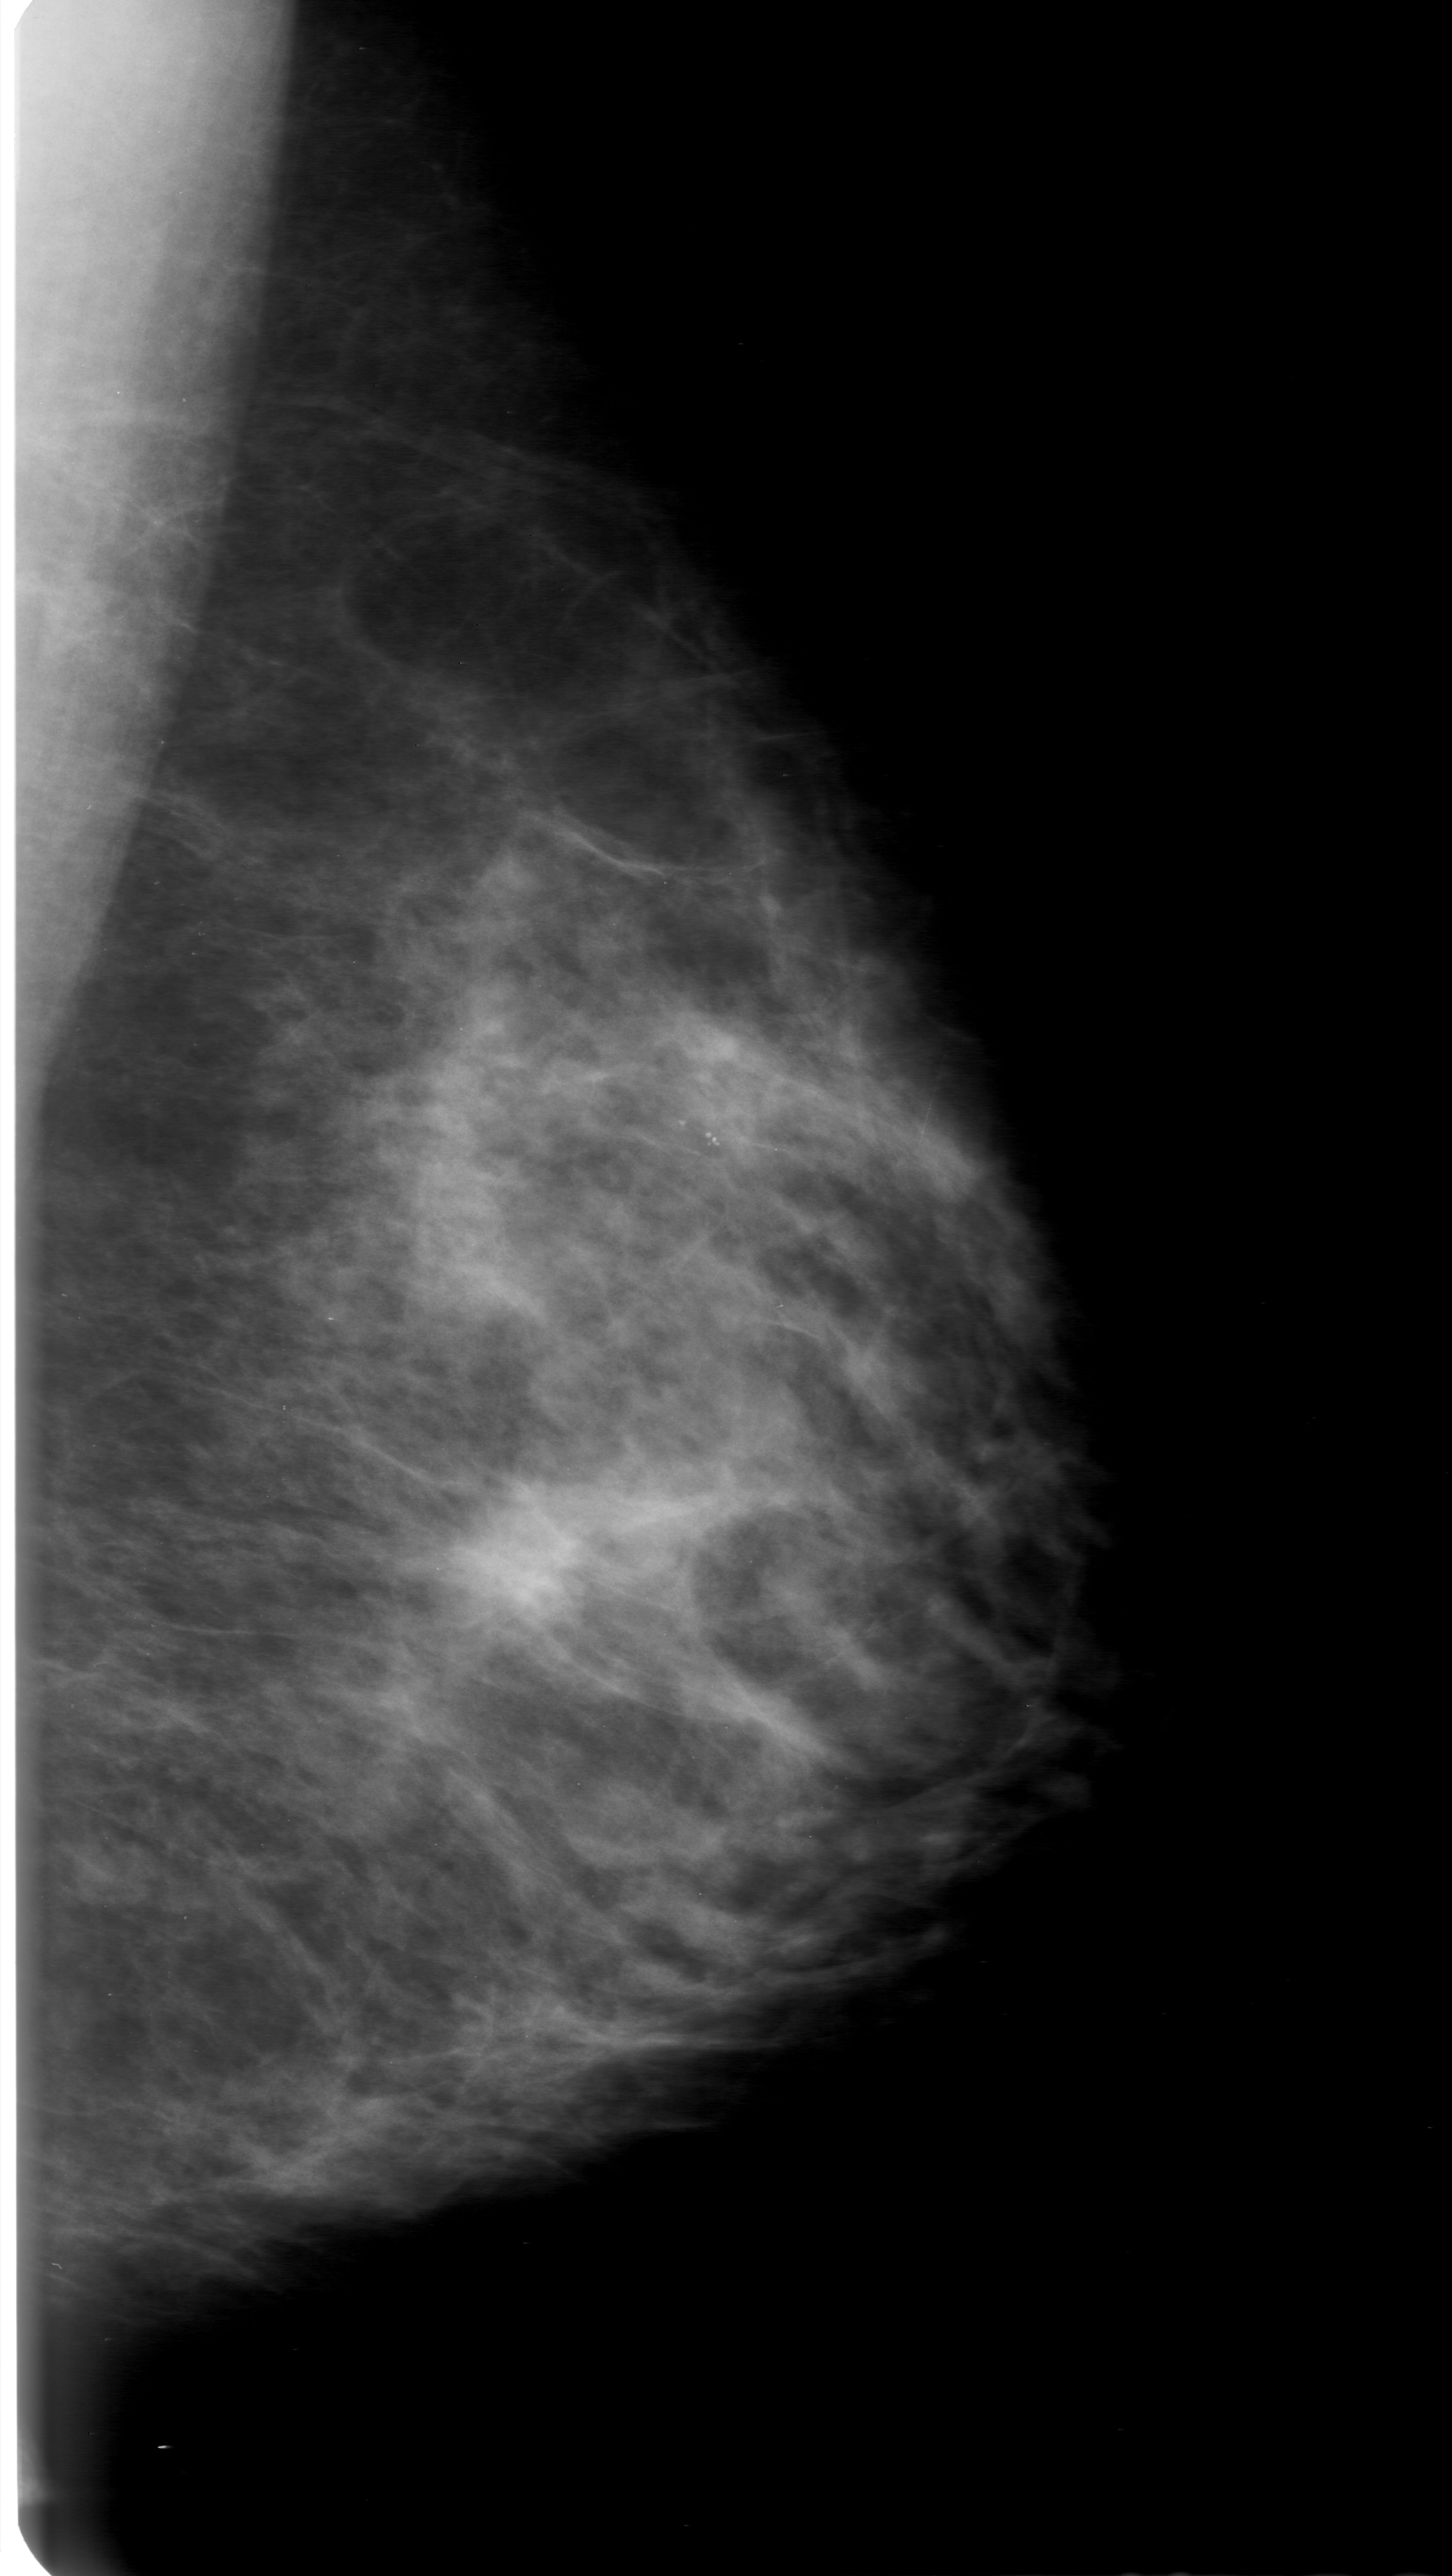
Scanned film-screen mammogram. Left breast. Mediolateral oblique (MLO) view. BI-RADS breast density category 3 (scale 1–4). 1452 × 2576 image matrix.
Marked abnormalities (boxes around the expert regions of interest):
- mass, shape oval, margins microlobulated; BI-RADS assessment category 0 (incomplete: needs additional imaging); subtlety rating 4 on a 1 (subtle) to 5 (obvious) scale; pathology (as recorded): malignant: box from (x=418, y=1465) to (x=596, y=1646) px